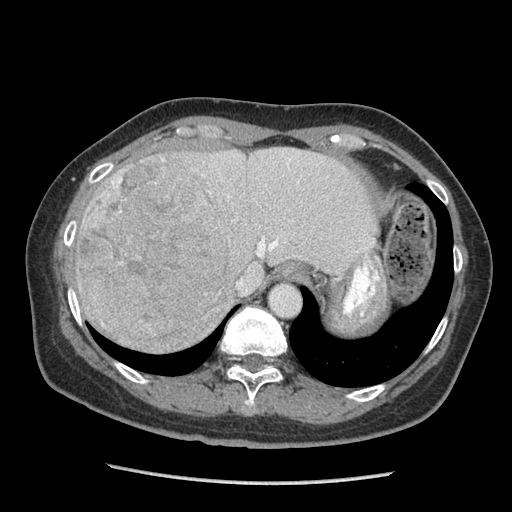
Contrast-enhanced abdominal CT (liver protocol), one axial slice. Slice 72 of 105 in the series (ordered by position). Reconstruction kernel STANDARD. Soft-tissue window (W 400 / L 40 HU). 2.5 mm slice thickness. 512 × 512 image matrix. Case-level facts recorded for this patient, not image findings: diagnosis: hepatocellular carcinoma (patient treated with transarterial chemoembolisation; whether this scan precedes or follows treatment is not stated here); TNM stage (as recorded): Stage-I; Child-Pugh class: A; tumour differentiation: moderately differentiated.
Outlined on this slice (semi-automatically segmented with operator editing):
- abdominal aorta: bounding box [x1, y1, x2, y2] px = [270, 284, 300, 317]
- liver parenchyma outside the tumour (the mass and vessels are separate outlines, so this box may not span the whole liver): [74, 146, 376, 334]
- mass: [75, 155, 229, 351]
- liver vessels: [228, 163, 299, 257]